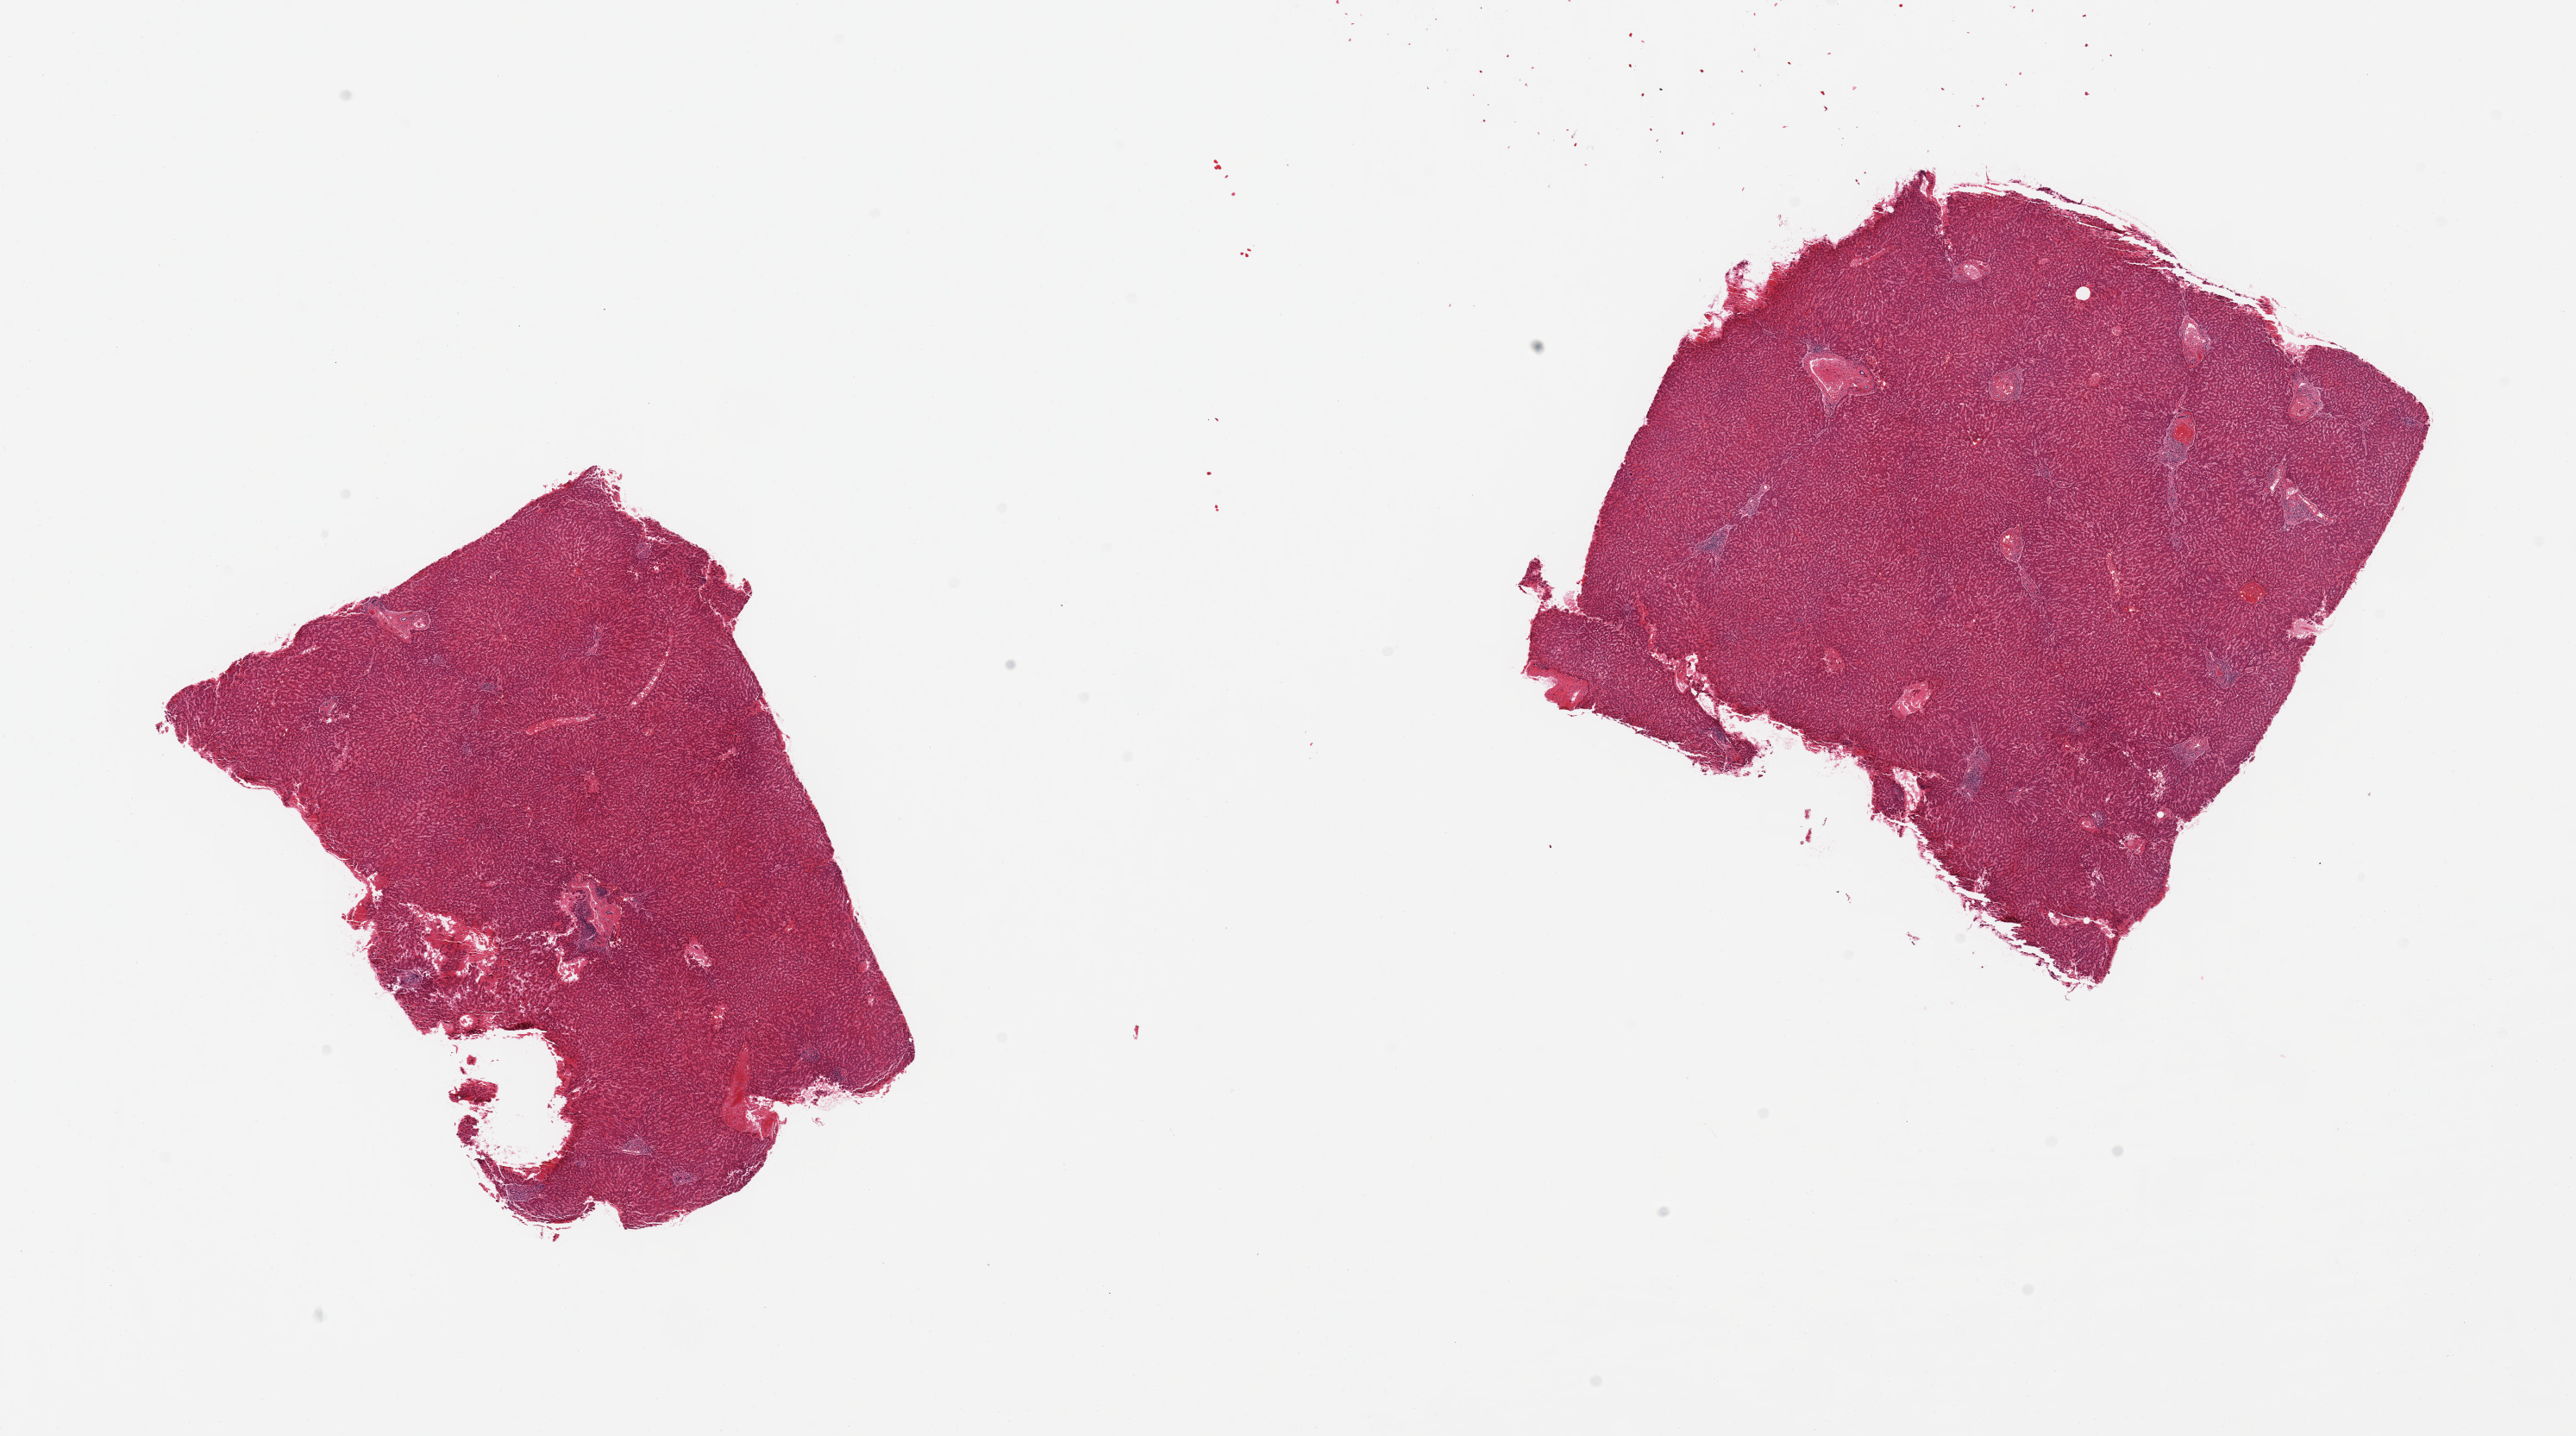
H&E whole-slide image, brightfield — shown as a low-resolution overview of the whole scanned area (about 23.6 x 13.2 mm, slide scanned at 20x). PAXgene-fixed, paraffin-embedded tissue. Sampled site (target tissue): liver. Tissue donor sample. Donor sex: male.
Pathologist's review note for this sample: 2 pieces; some congestion and portal chronic inflammation.